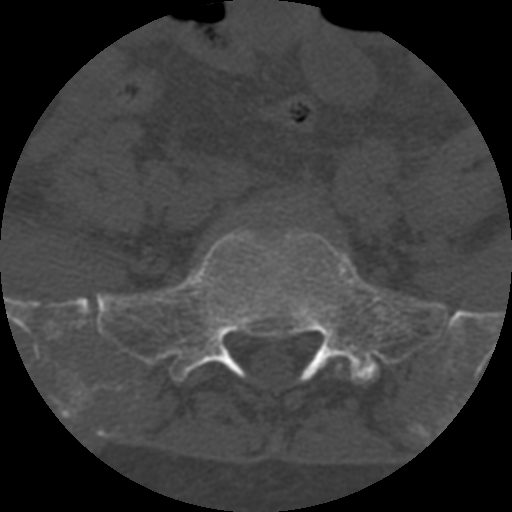
CT including the spine, one axial slice; position 170 of 708 along the scan axis; reconstruction kernel STANDARD; one of 3 acquisitions stored at this slice position; bone window (W 1800 / L 400 HU); 1.25 mm slice thickness; 512 × 512 image matrix. Patient age 55 years. Case-level facts recorded for this patient, not image findings: primary cancer: colon; vertebrae with lytic lesions (as recorded): T12, L1, L5.
Structures marked on this image (semi-automatically segmented with operator editing):
- L5 vertebra: bounding box [x1, y1, x2, y2] px = [336, 364, 343, 374]